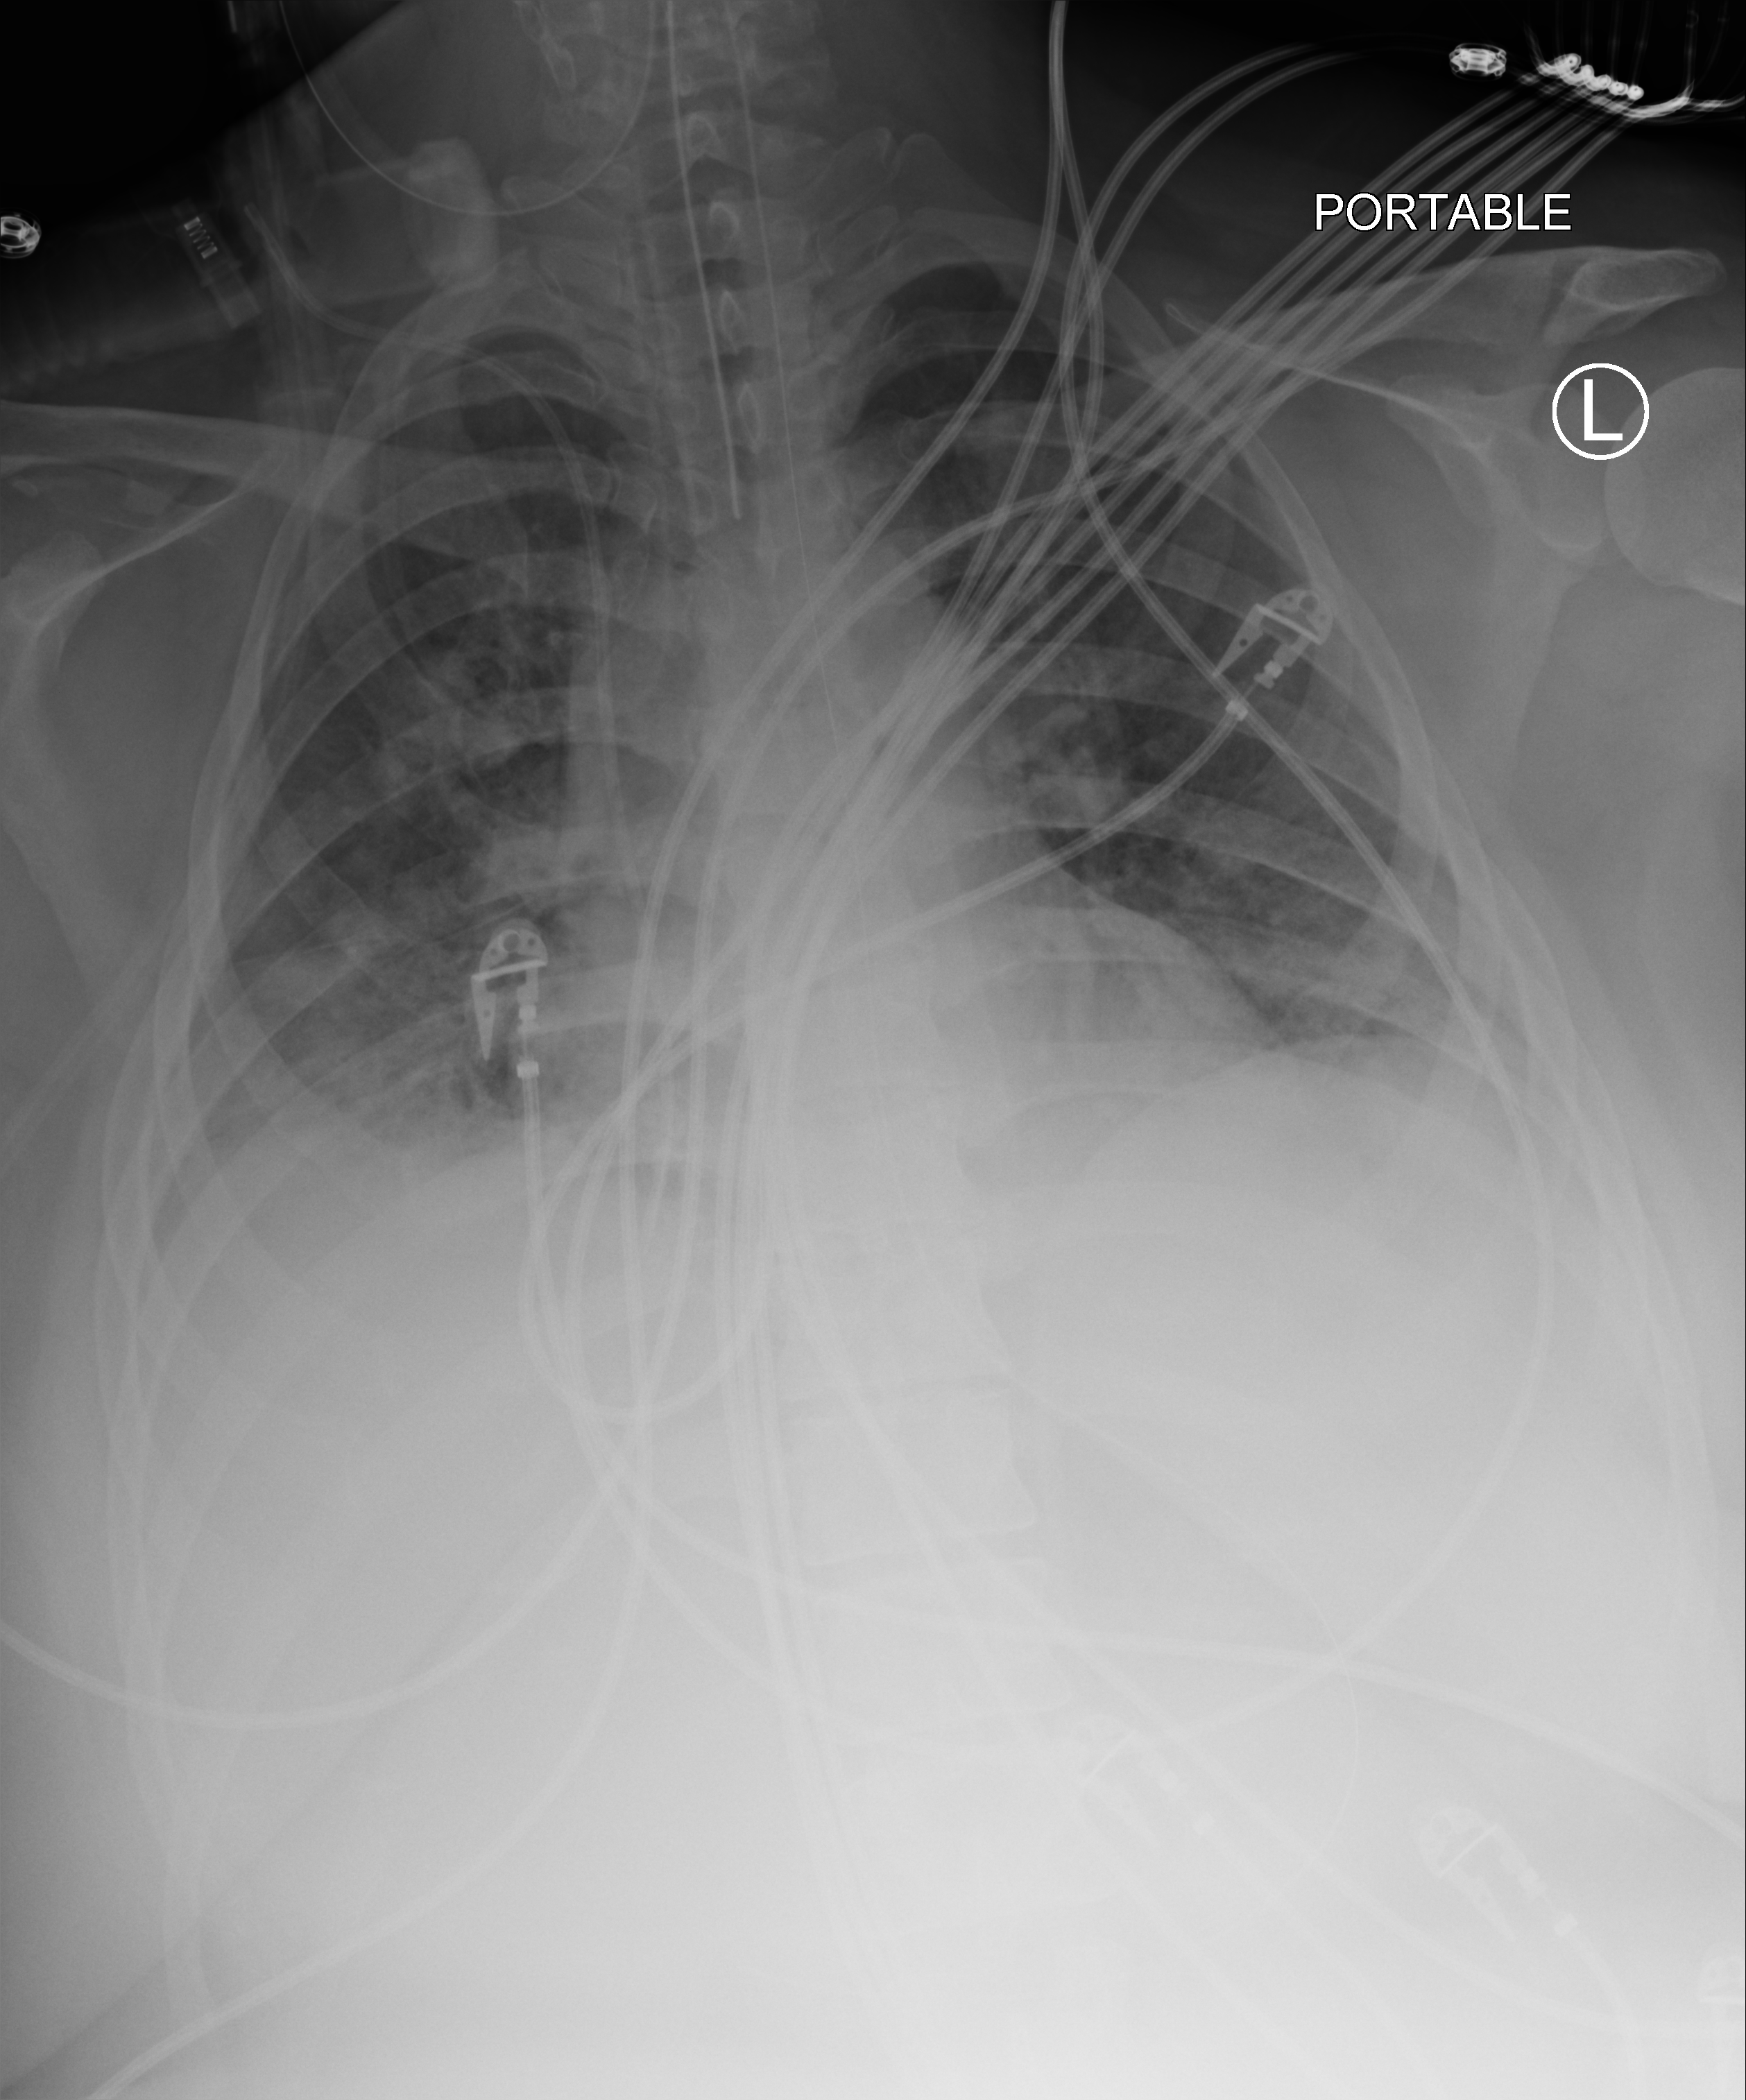
Chest X-ray (portable); anteroposterior (AP) projection. Patient hospitalised with COVID-19; female, aged 18–59 years.
Hospital-stay facts (about this admission, not read from this image; timing relative to this image not recorded):
- admitted to intensive care during this hospital stay: yes